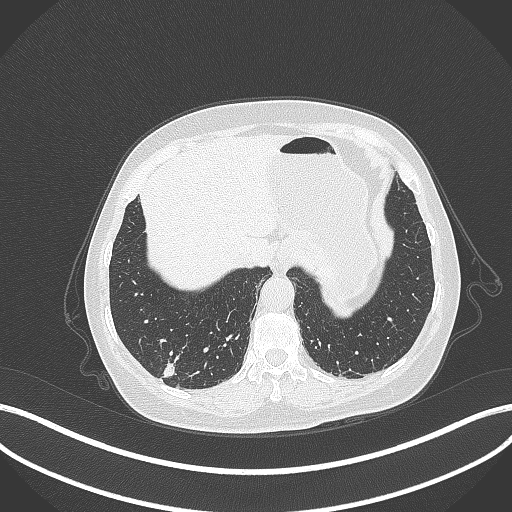
Chest CT, one axial slice; position 47 of 333 along the scan axis; reconstruction kernel B70f; 120 kVp; lung window (W 1500 / L -600 HU); 1 mm slice thickness; 512 × 512 image matrix, field of view 400 × 400 mm. Patient: female, 69 years. Case-level facts recorded for this patient, not image findings: clinical TNM (as recorded): T1b N0 M0; histopathological grade: G2-3.
Annotated regions visible in this slice (rectangle marked by the reading radiologist):
- lung tumour (recorded histology: adenocarcinoma): bounding box <156,357,180,379> (left, top, right, bottom; pixels)